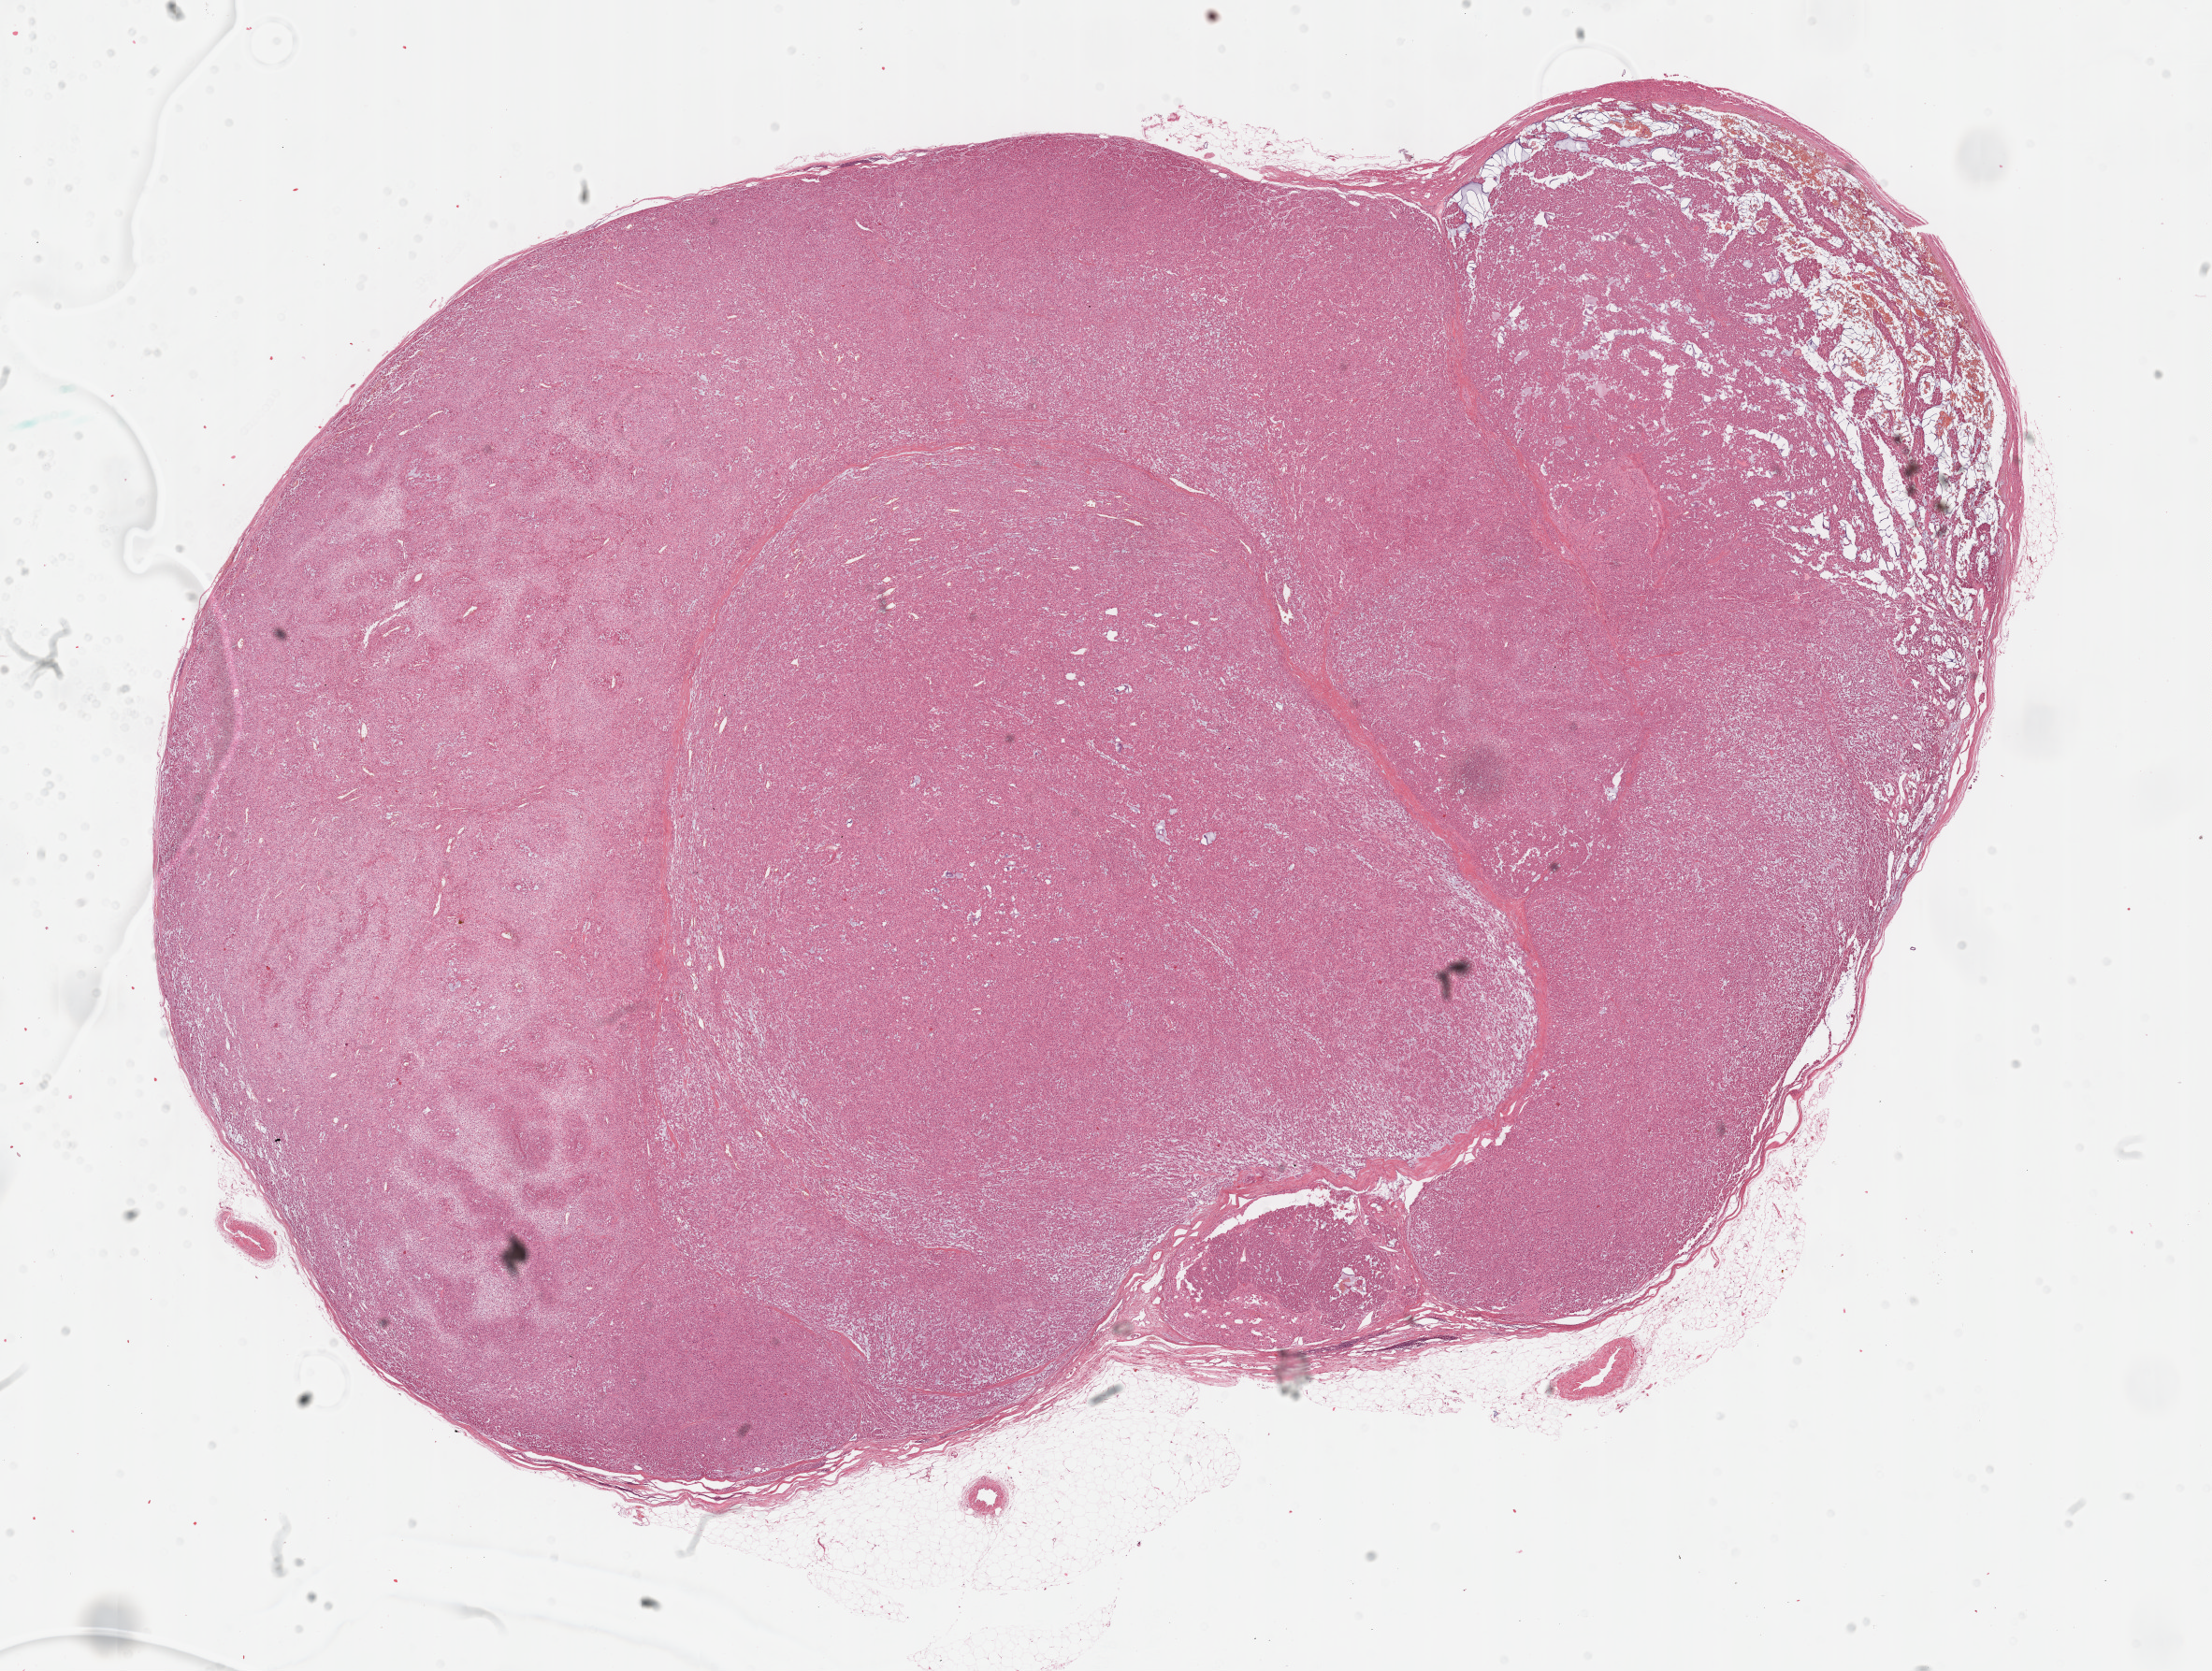
H&E whole-slide image — shown as a low-resolution overview of the whole scanned area (about 19.1 x 14.5 mm, slide scanned at 40x), formalin-fixed paraffin-embedded (FFPE) diagnostic section, primary tumour sample from the adrenal cortex. Male patient; age at initial diagnosis 61 years.
Pathologic diagnosis: Adrenal cortical carcinoma (cortex of adrenal gland). Laterality: left.